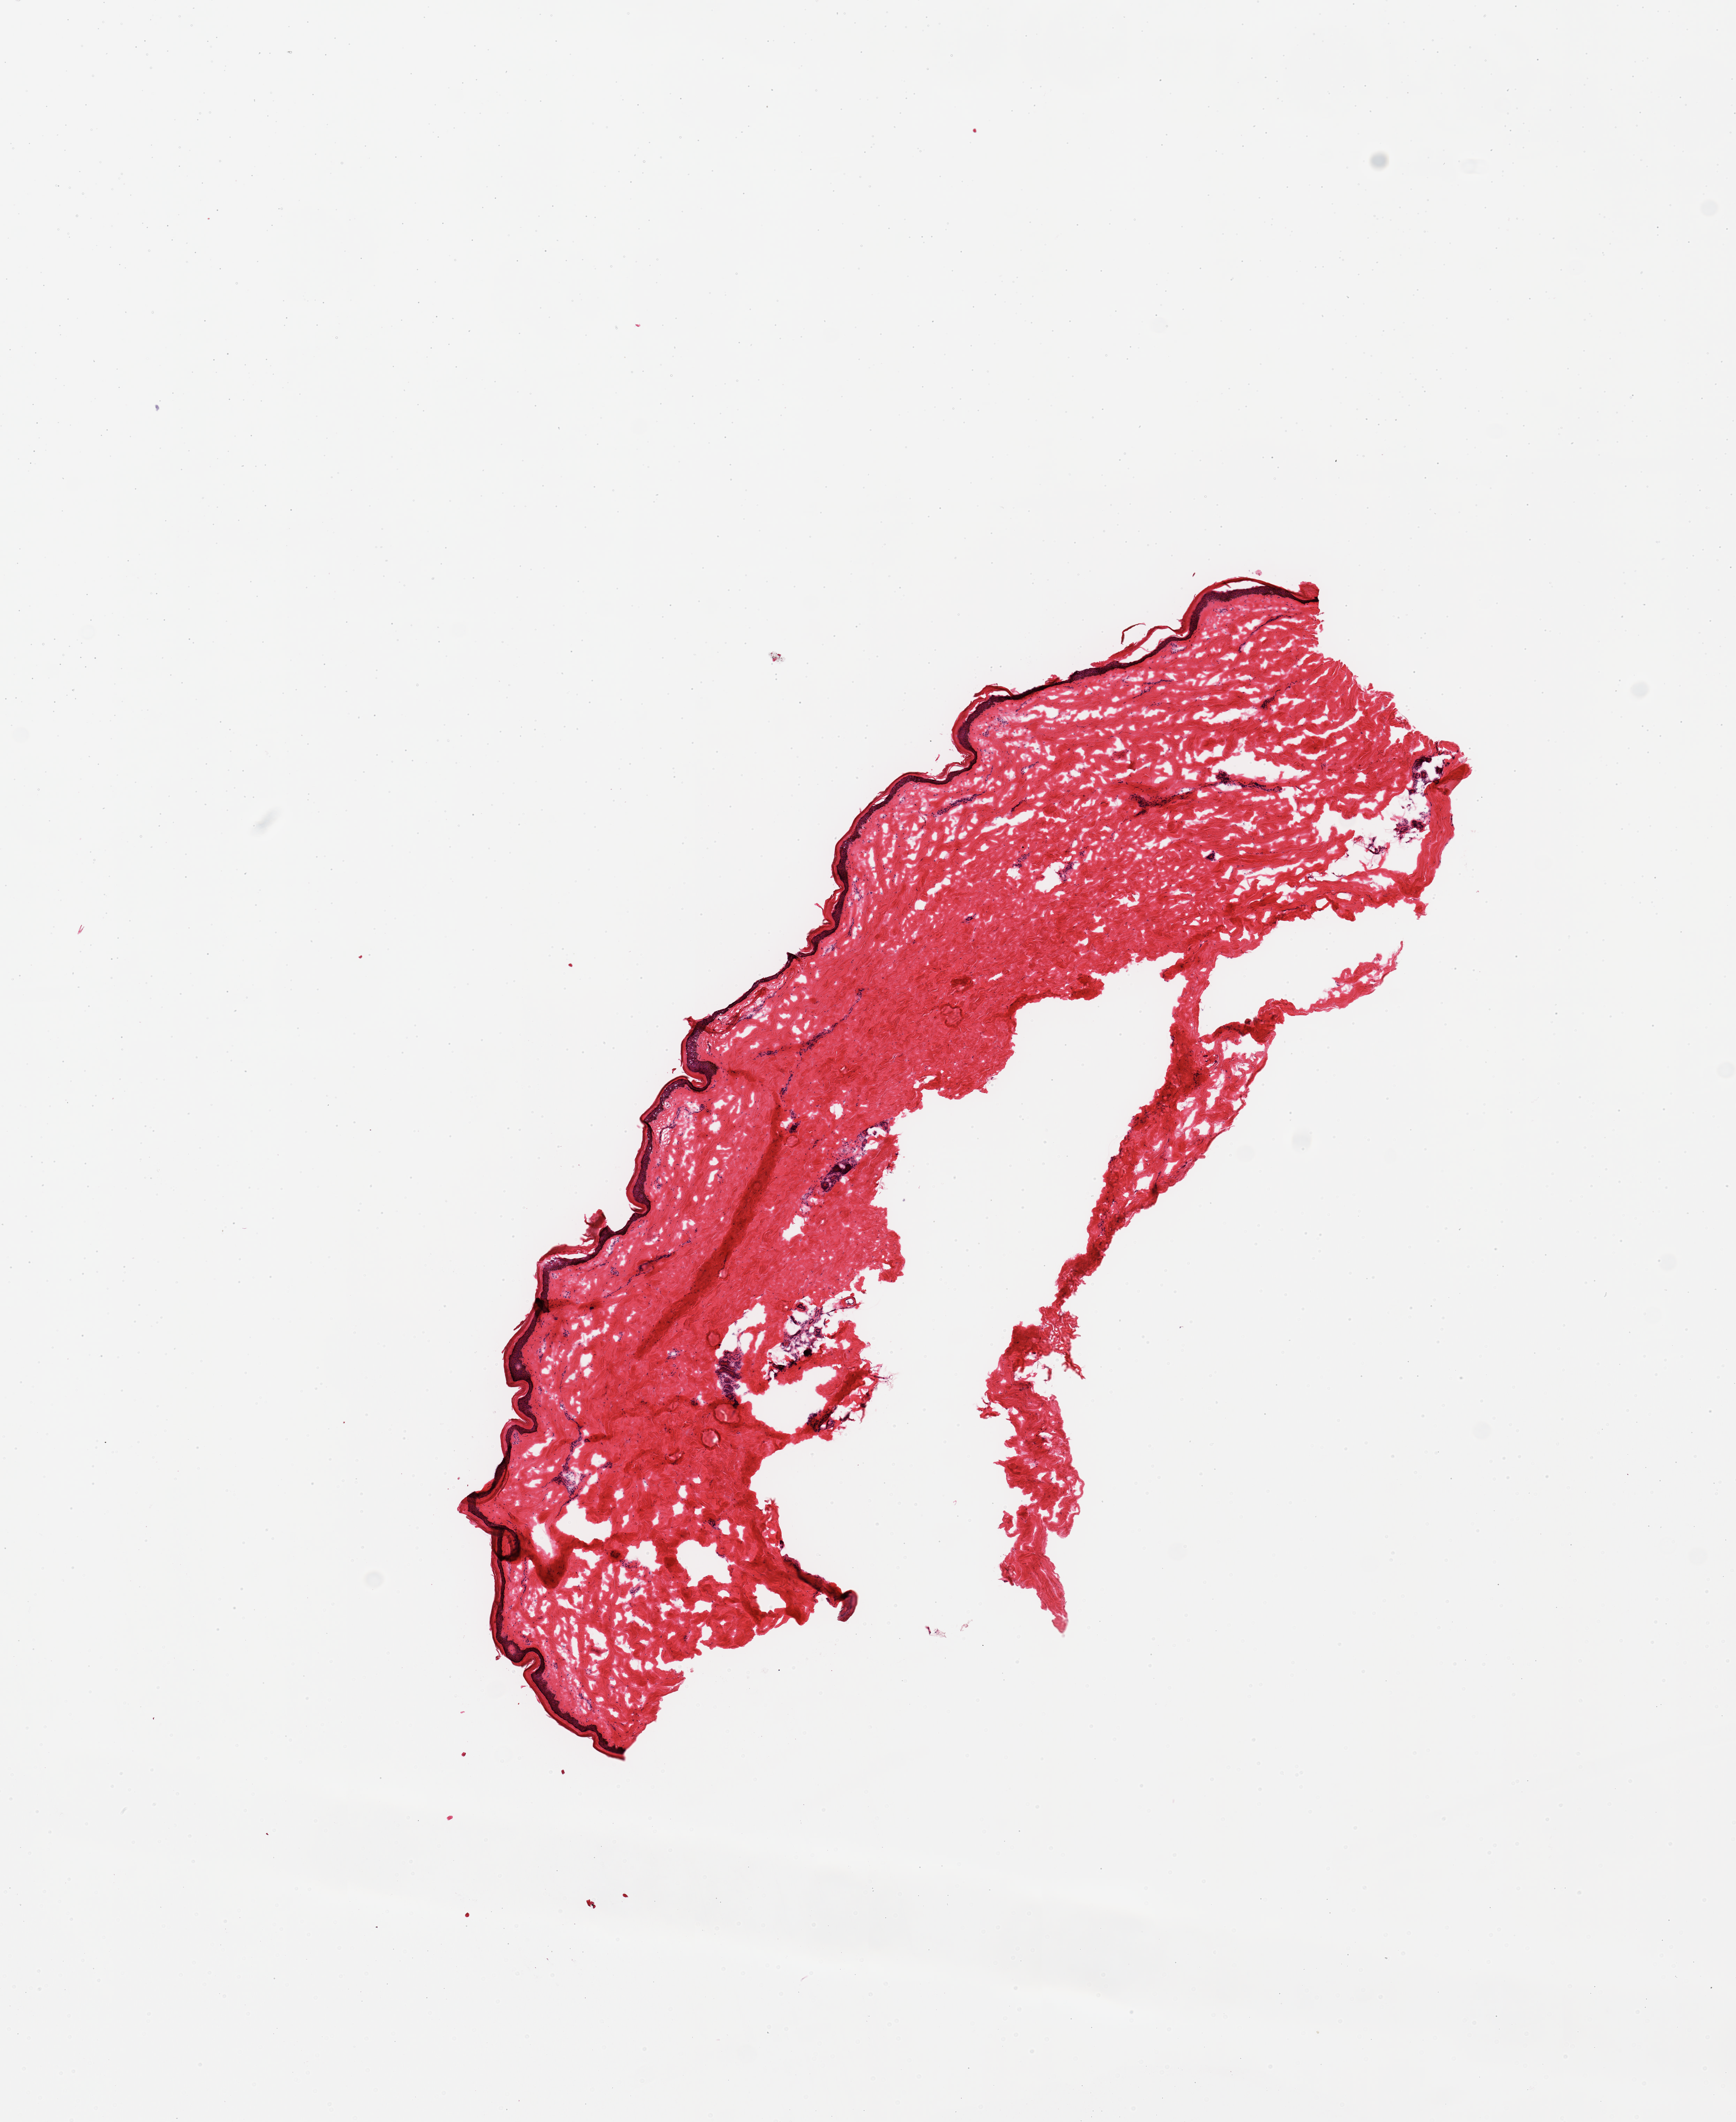
Digitized hematoxylin and eosin (H&E)-stained section, whole scanned area (about 9.8 x 12.0 mm, from a 20x scan) shown as a low-resolution overview. Female donor.
Specimen: frozen section (dry ice); section of skin of lower leg (target tissue); donor tissue sample.